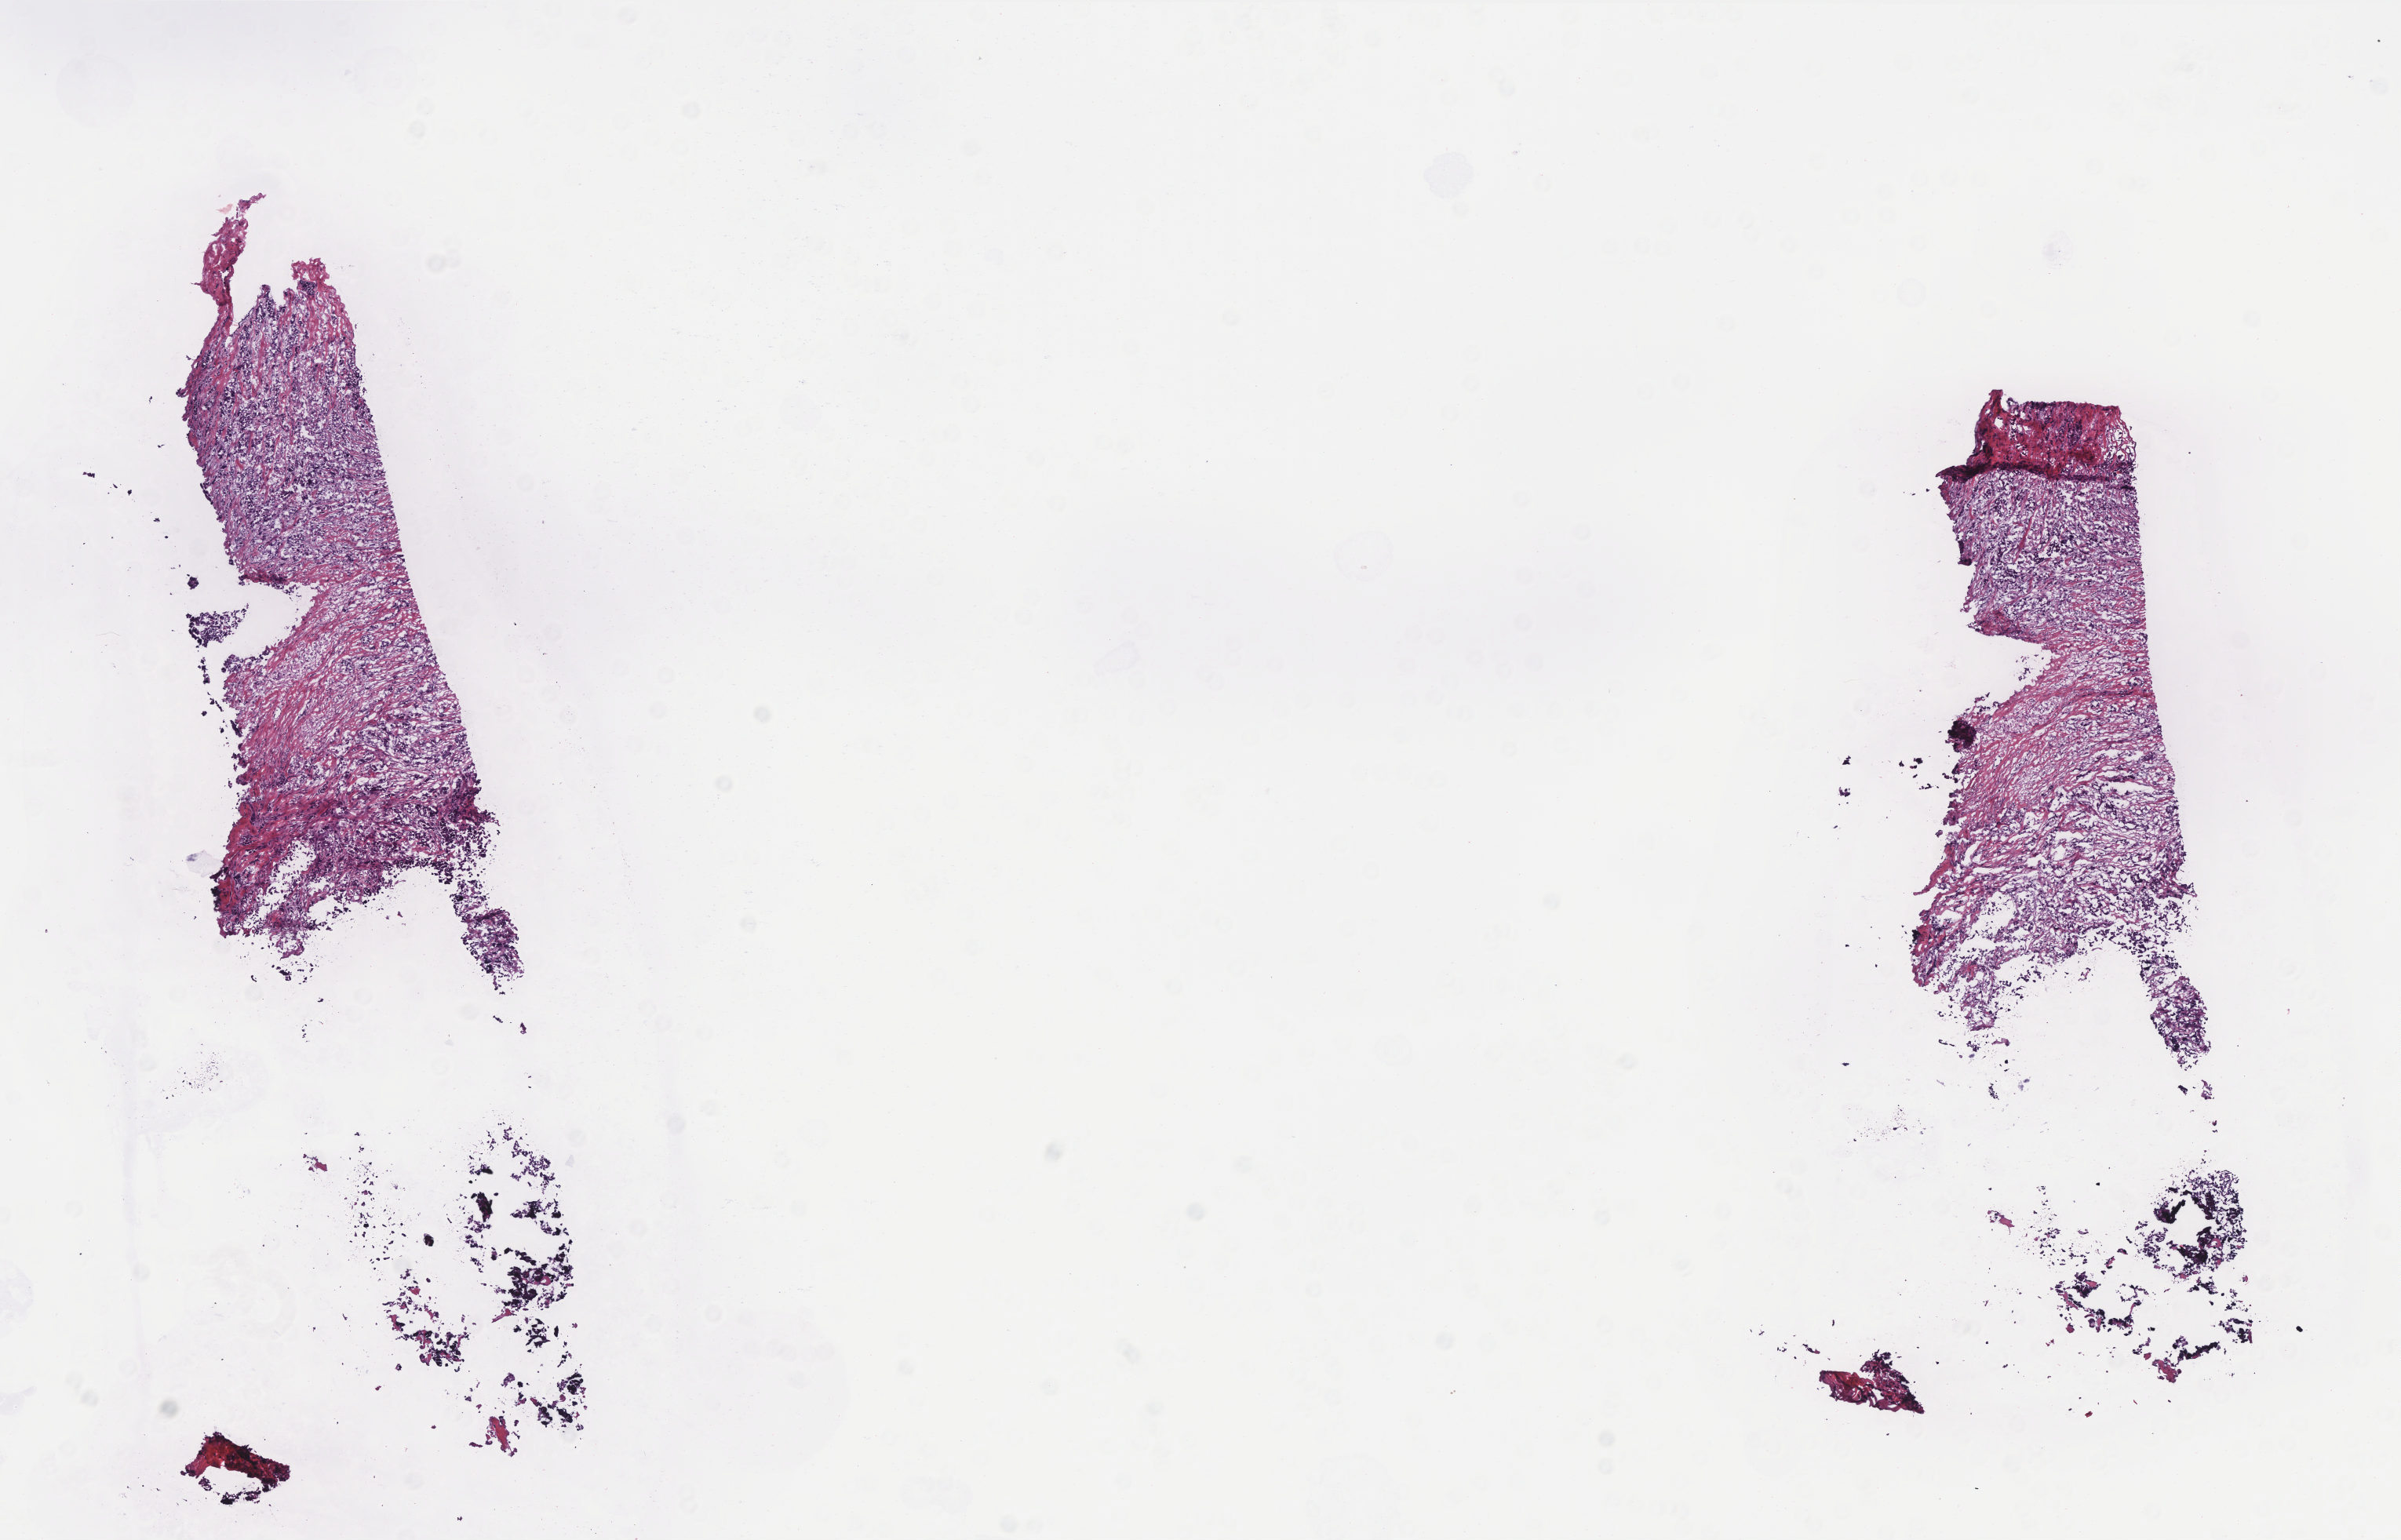
Whole-slide histology image, Hematoxylin and eosin (H&E) stained, a low-resolution overview of the entire scanned area, about 12.3 x 7.9 mm. Frozen section. Sample: primary tumour, breast. Female patient; age at initial diagnosis 74 years. Composition of this section per pathologist review: tumour cells 80%, tumour nuclei 80%, normal cells 0%, stromal cells 19%, necrosis 1%. Infiltration values recorded for this section: lymphocyte infiltration 0%, monocyte infiltration 0%, neutrophil infiltration 0%.
* lymph nodes positive (case pathology): 0 of 19 examined
* AJCC pathologic stage: IIA
* histologic diagnosis: Infiltrating duct carcinoma, NOS
* TNM: T2 N0 M0